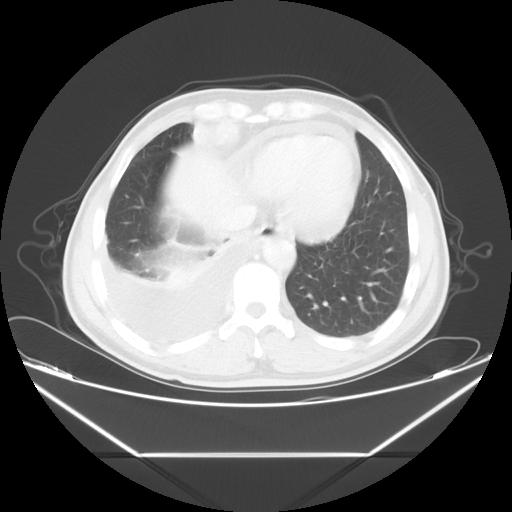
Chest CT, one axial slice. Slice 13 of 56 in the series (ordered by position). Reconstruction kernel STANDARD. 120 kVp. Lung window (W 1500 / L -600 HU). 5 mm slice thickness. 512 × 512 image matrix, field of view 412 × 412 mm. Male patient, age 57 years. Case-level facts recorded for this patient, not image findings: clinical TNM (as recorded): T2 N3 M1.
Annotated regions visible in this slice (bounding box drawn by a radiologist):
- lung tumour (recorded histology: adenocarcinoma): box from (x=181, y=117) to (x=241, y=153) px